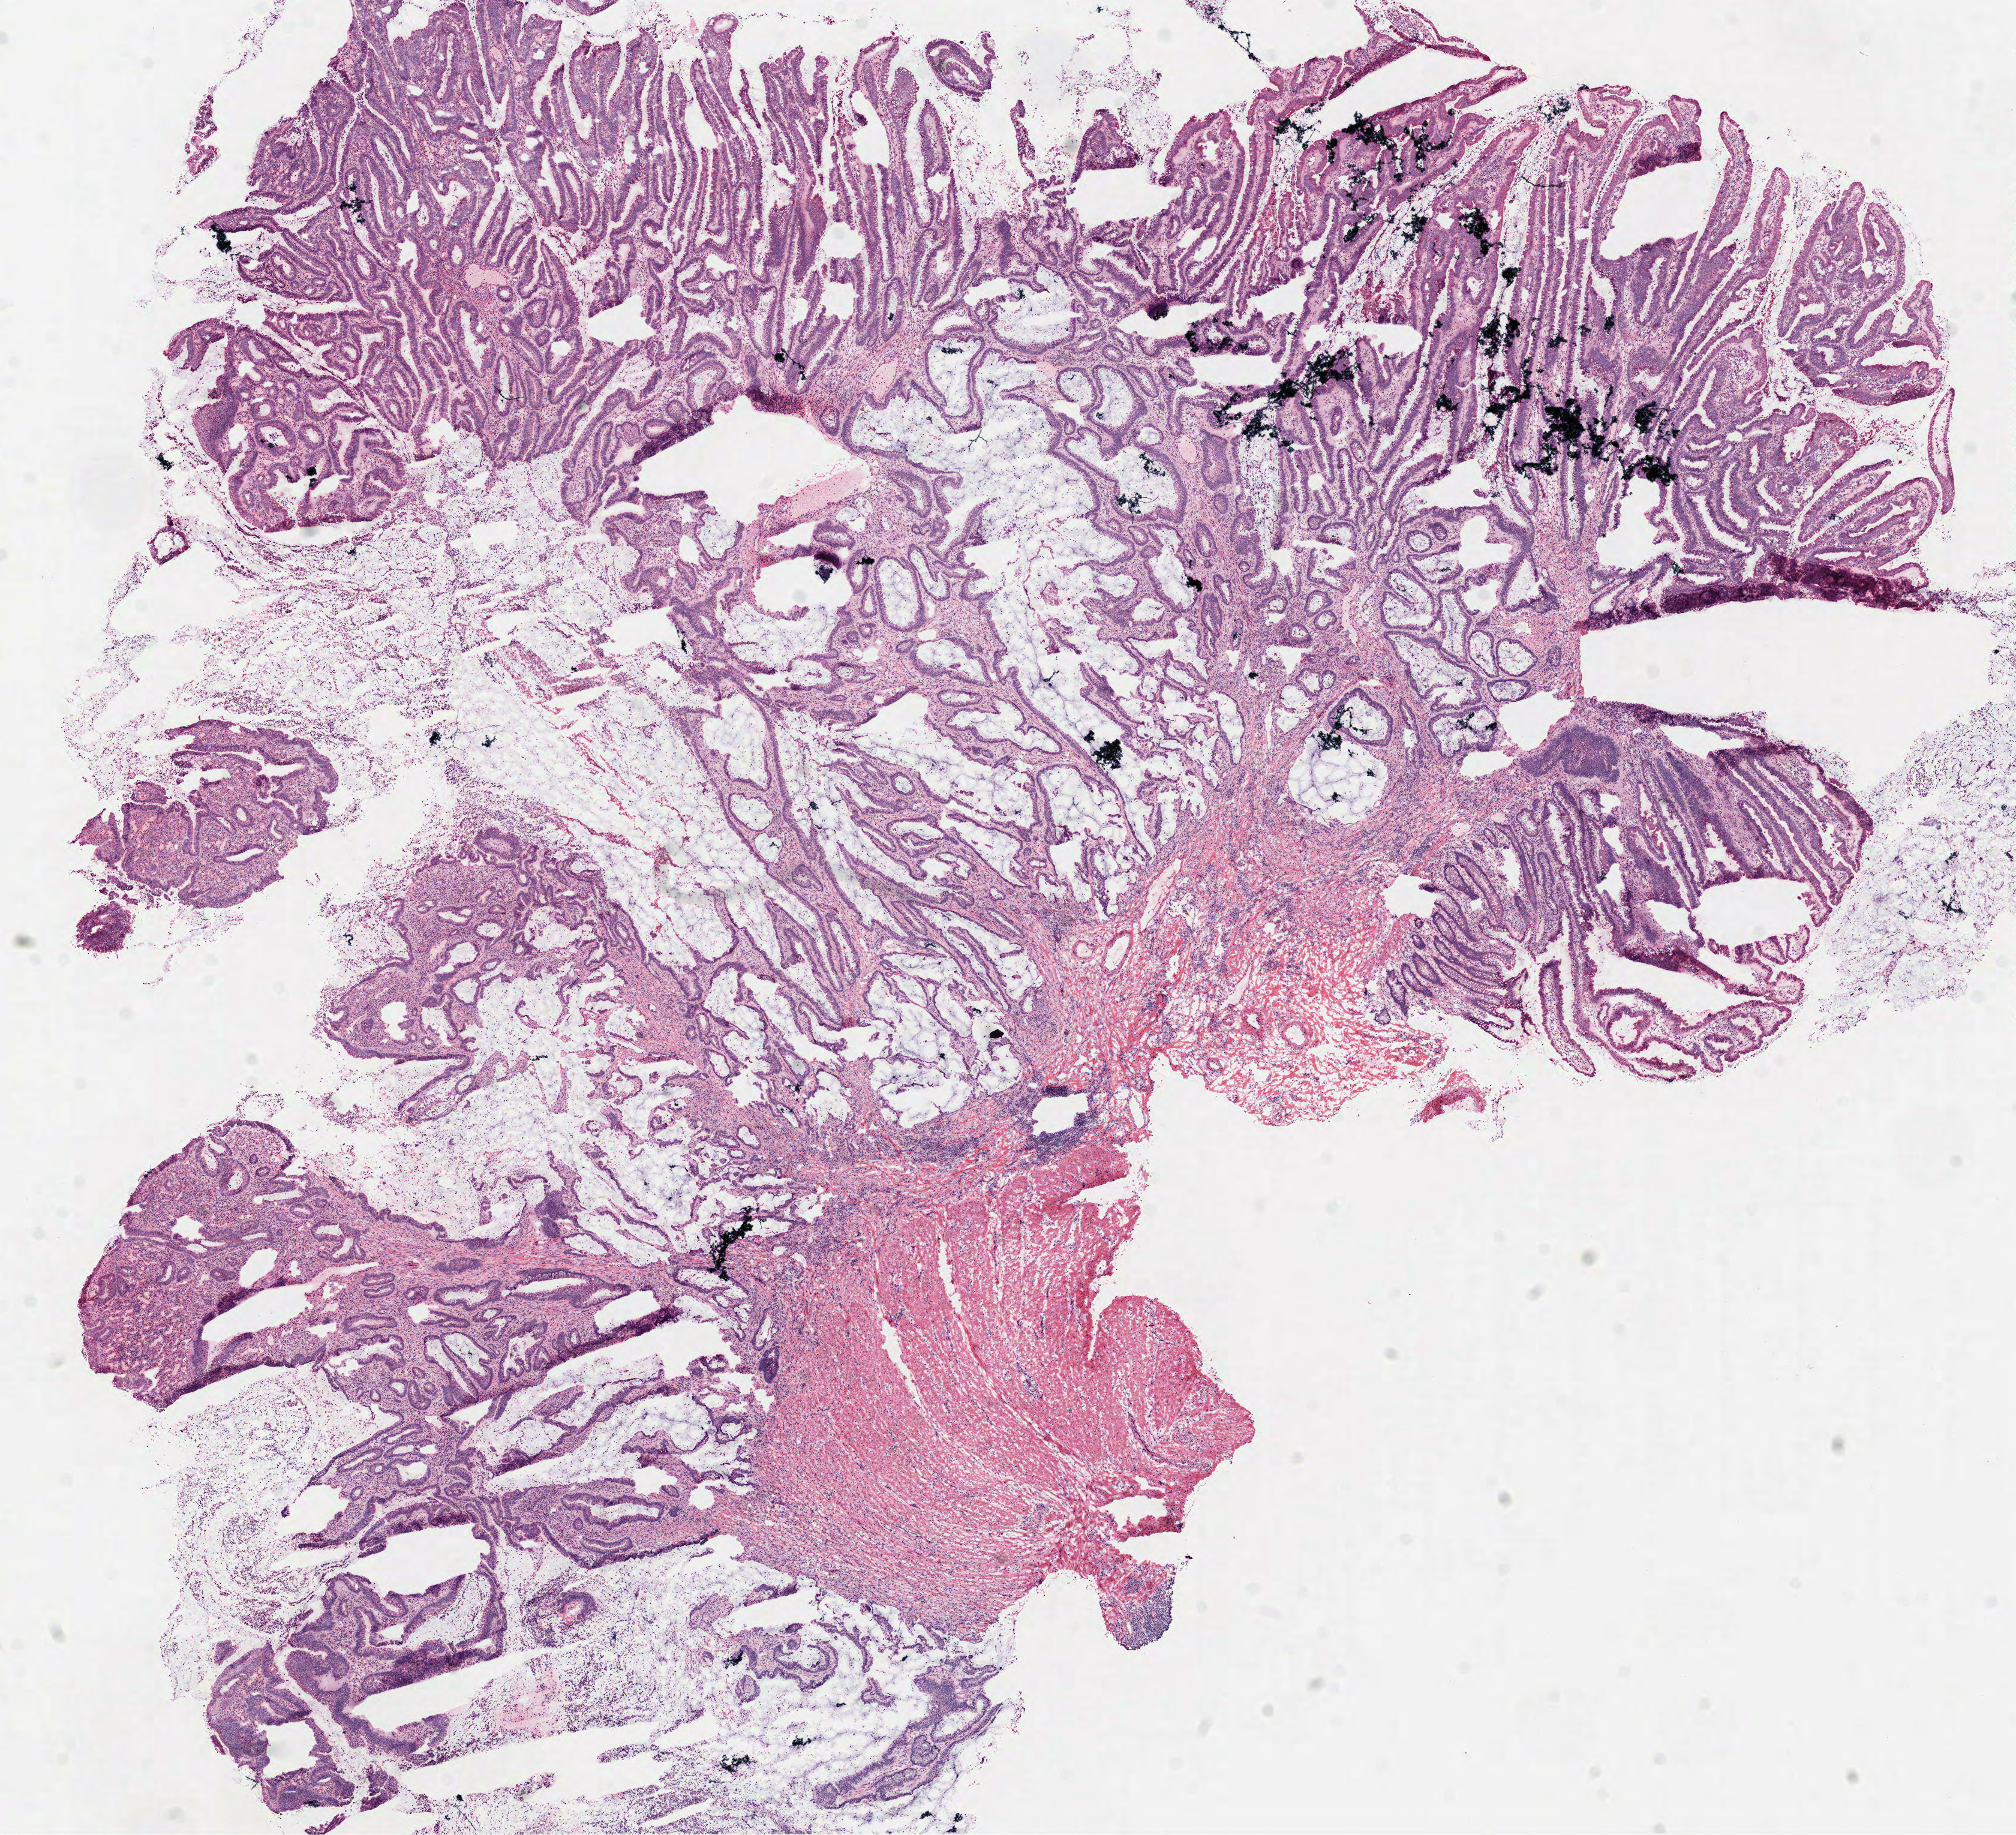
Whole-slide histology image, H&E-stained — whole scanned area (about 13.6 x 12.3 mm, slide scanned at 40x) shown as a low-resolution overview. Frozen section. Primary tumour sample from the colon. Male patient; age at initial diagnosis 39 years. Composition of this section per pathologist review: tumour cells 65%, tumour nuclei 80%, normal cells 10%, stromal cells 15%, necrosis 10%.
AJCC pathologic stage: IIA. TNM: T3 N0 M0. Diagnosis: Adenocarcinoma, NOS (hepatic flexure of colon). Lymph nodes positive (case pathology): 0 of 43 examined.